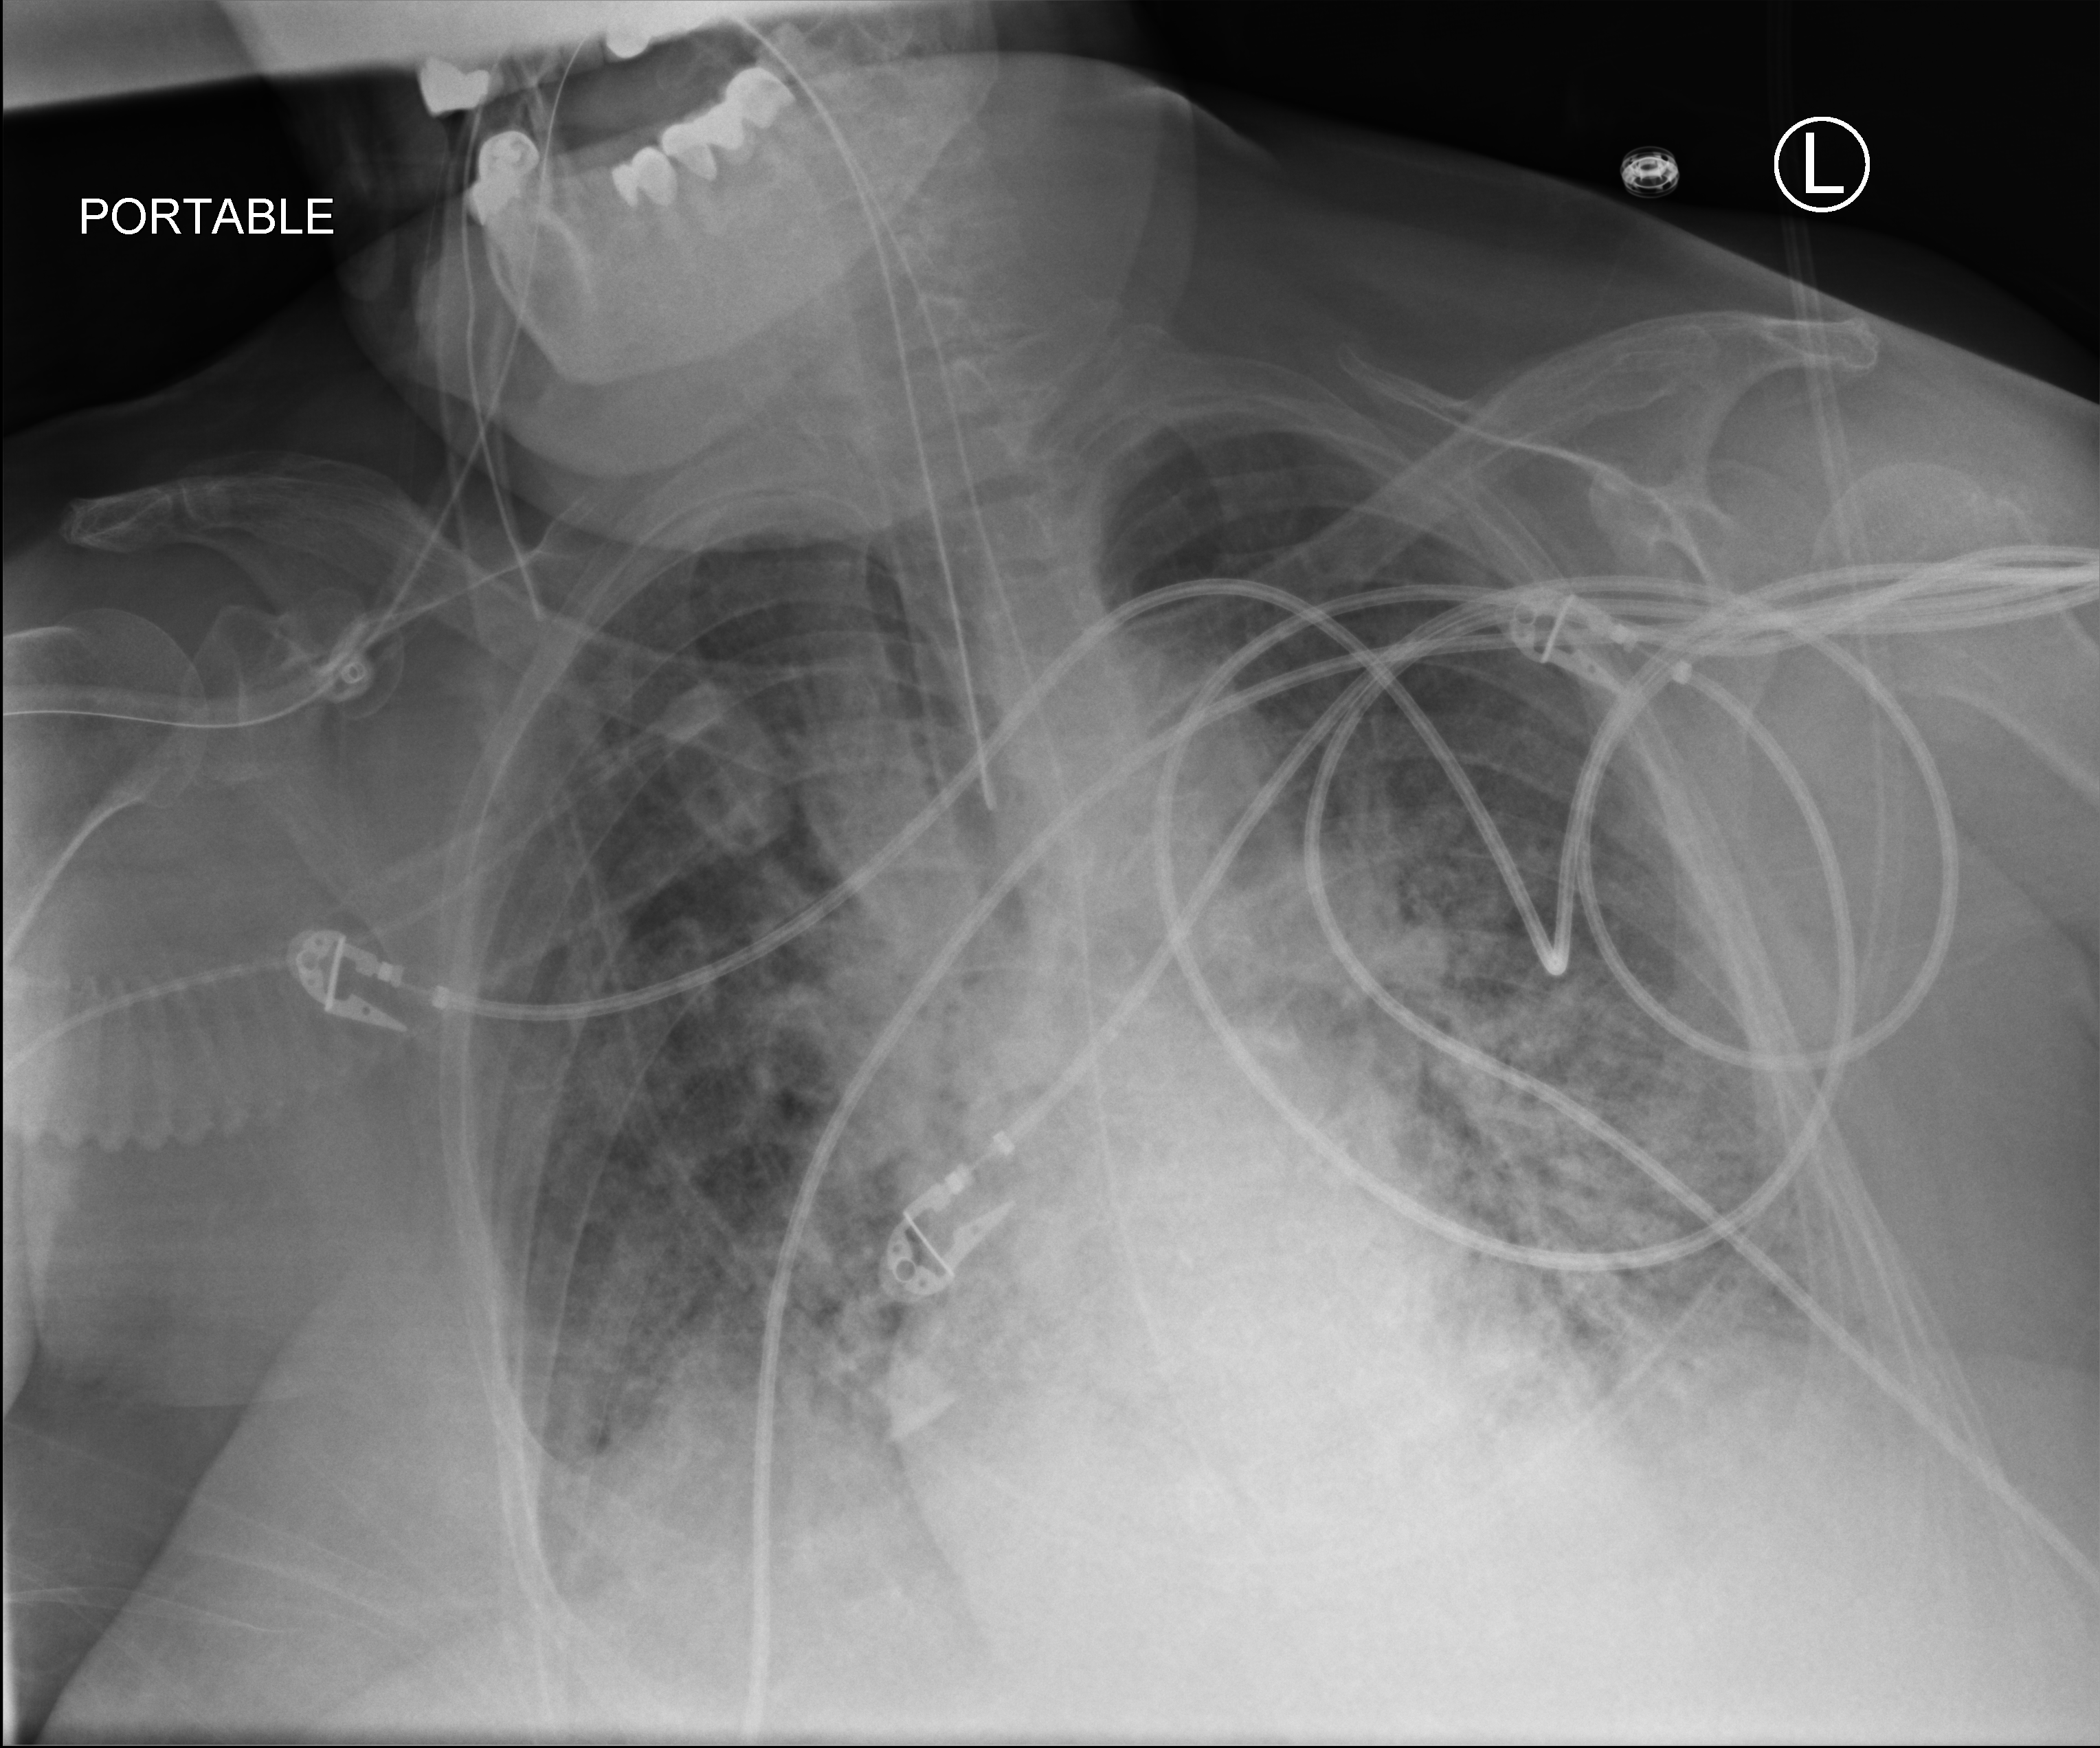
Bedside chest radiograph (computed radiography); anteroposterior (AP) projection. Female patient hospitalised with COVID-19, age 60–74 years.
Admission-level facts for this patient (not findings on this image; timing relative to this image not recorded):
- length of hospital stay: 15 days
- mechanically ventilated during this hospital stay: yes
- other chronic lung disease (admission record): no